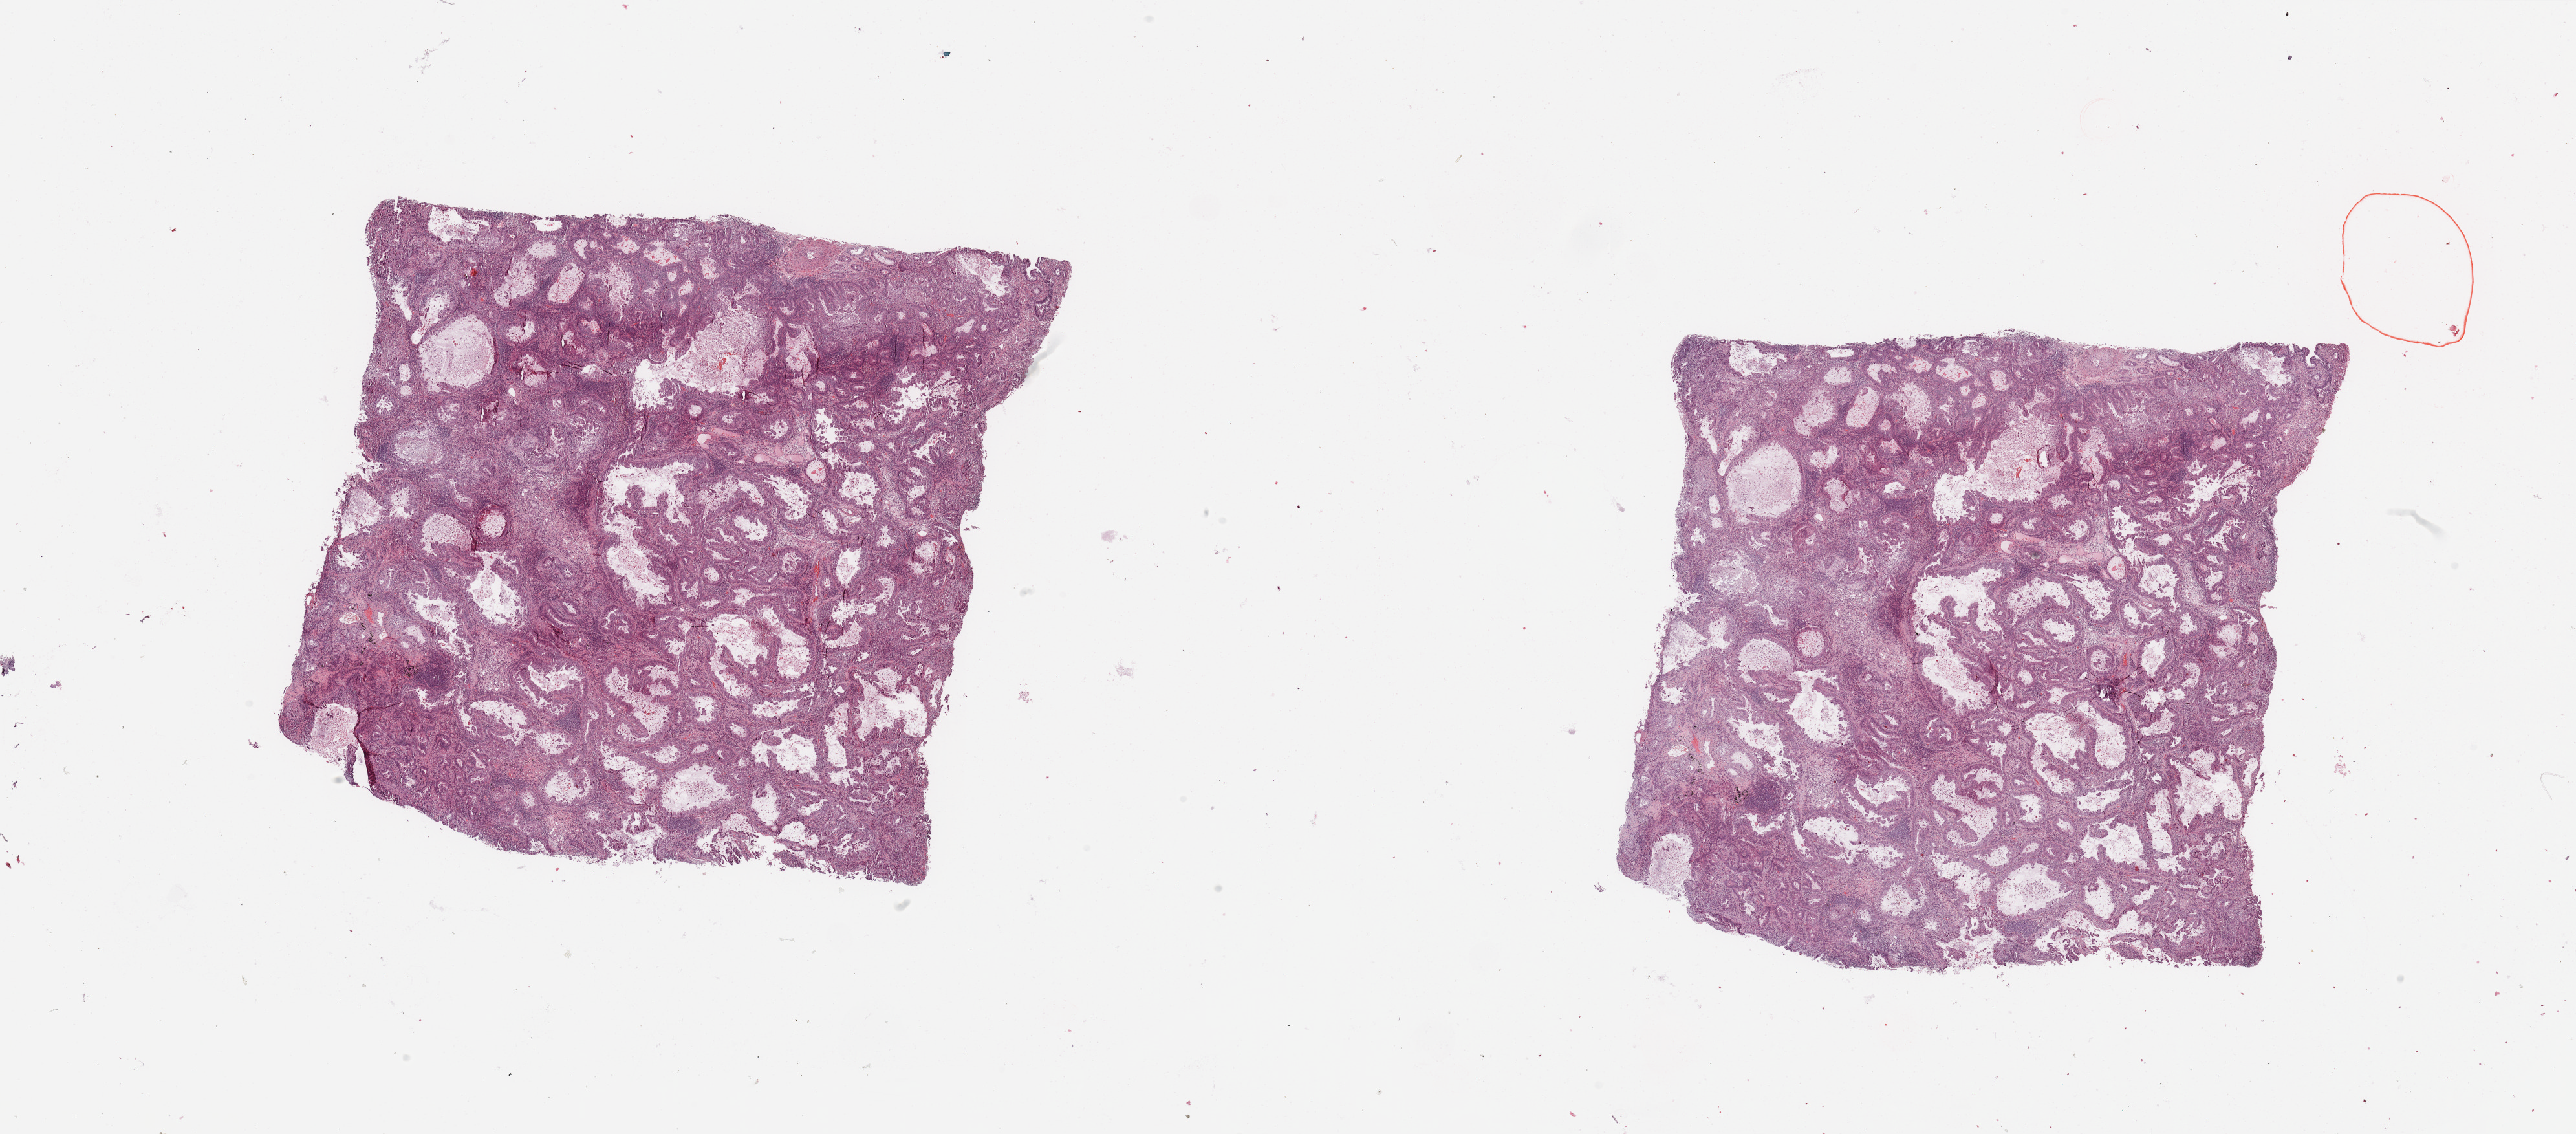
Hematoxylin and eosin (H&E) stained whole-slide image, whole scanned area (about 31.5 x 13.9 mm, acquisition: 20x scan) shown as a low-resolution overview; lung, tissue type not recorded.
• patient diagnosis (cohort enrolment): lung adenocarcinoma (lung)